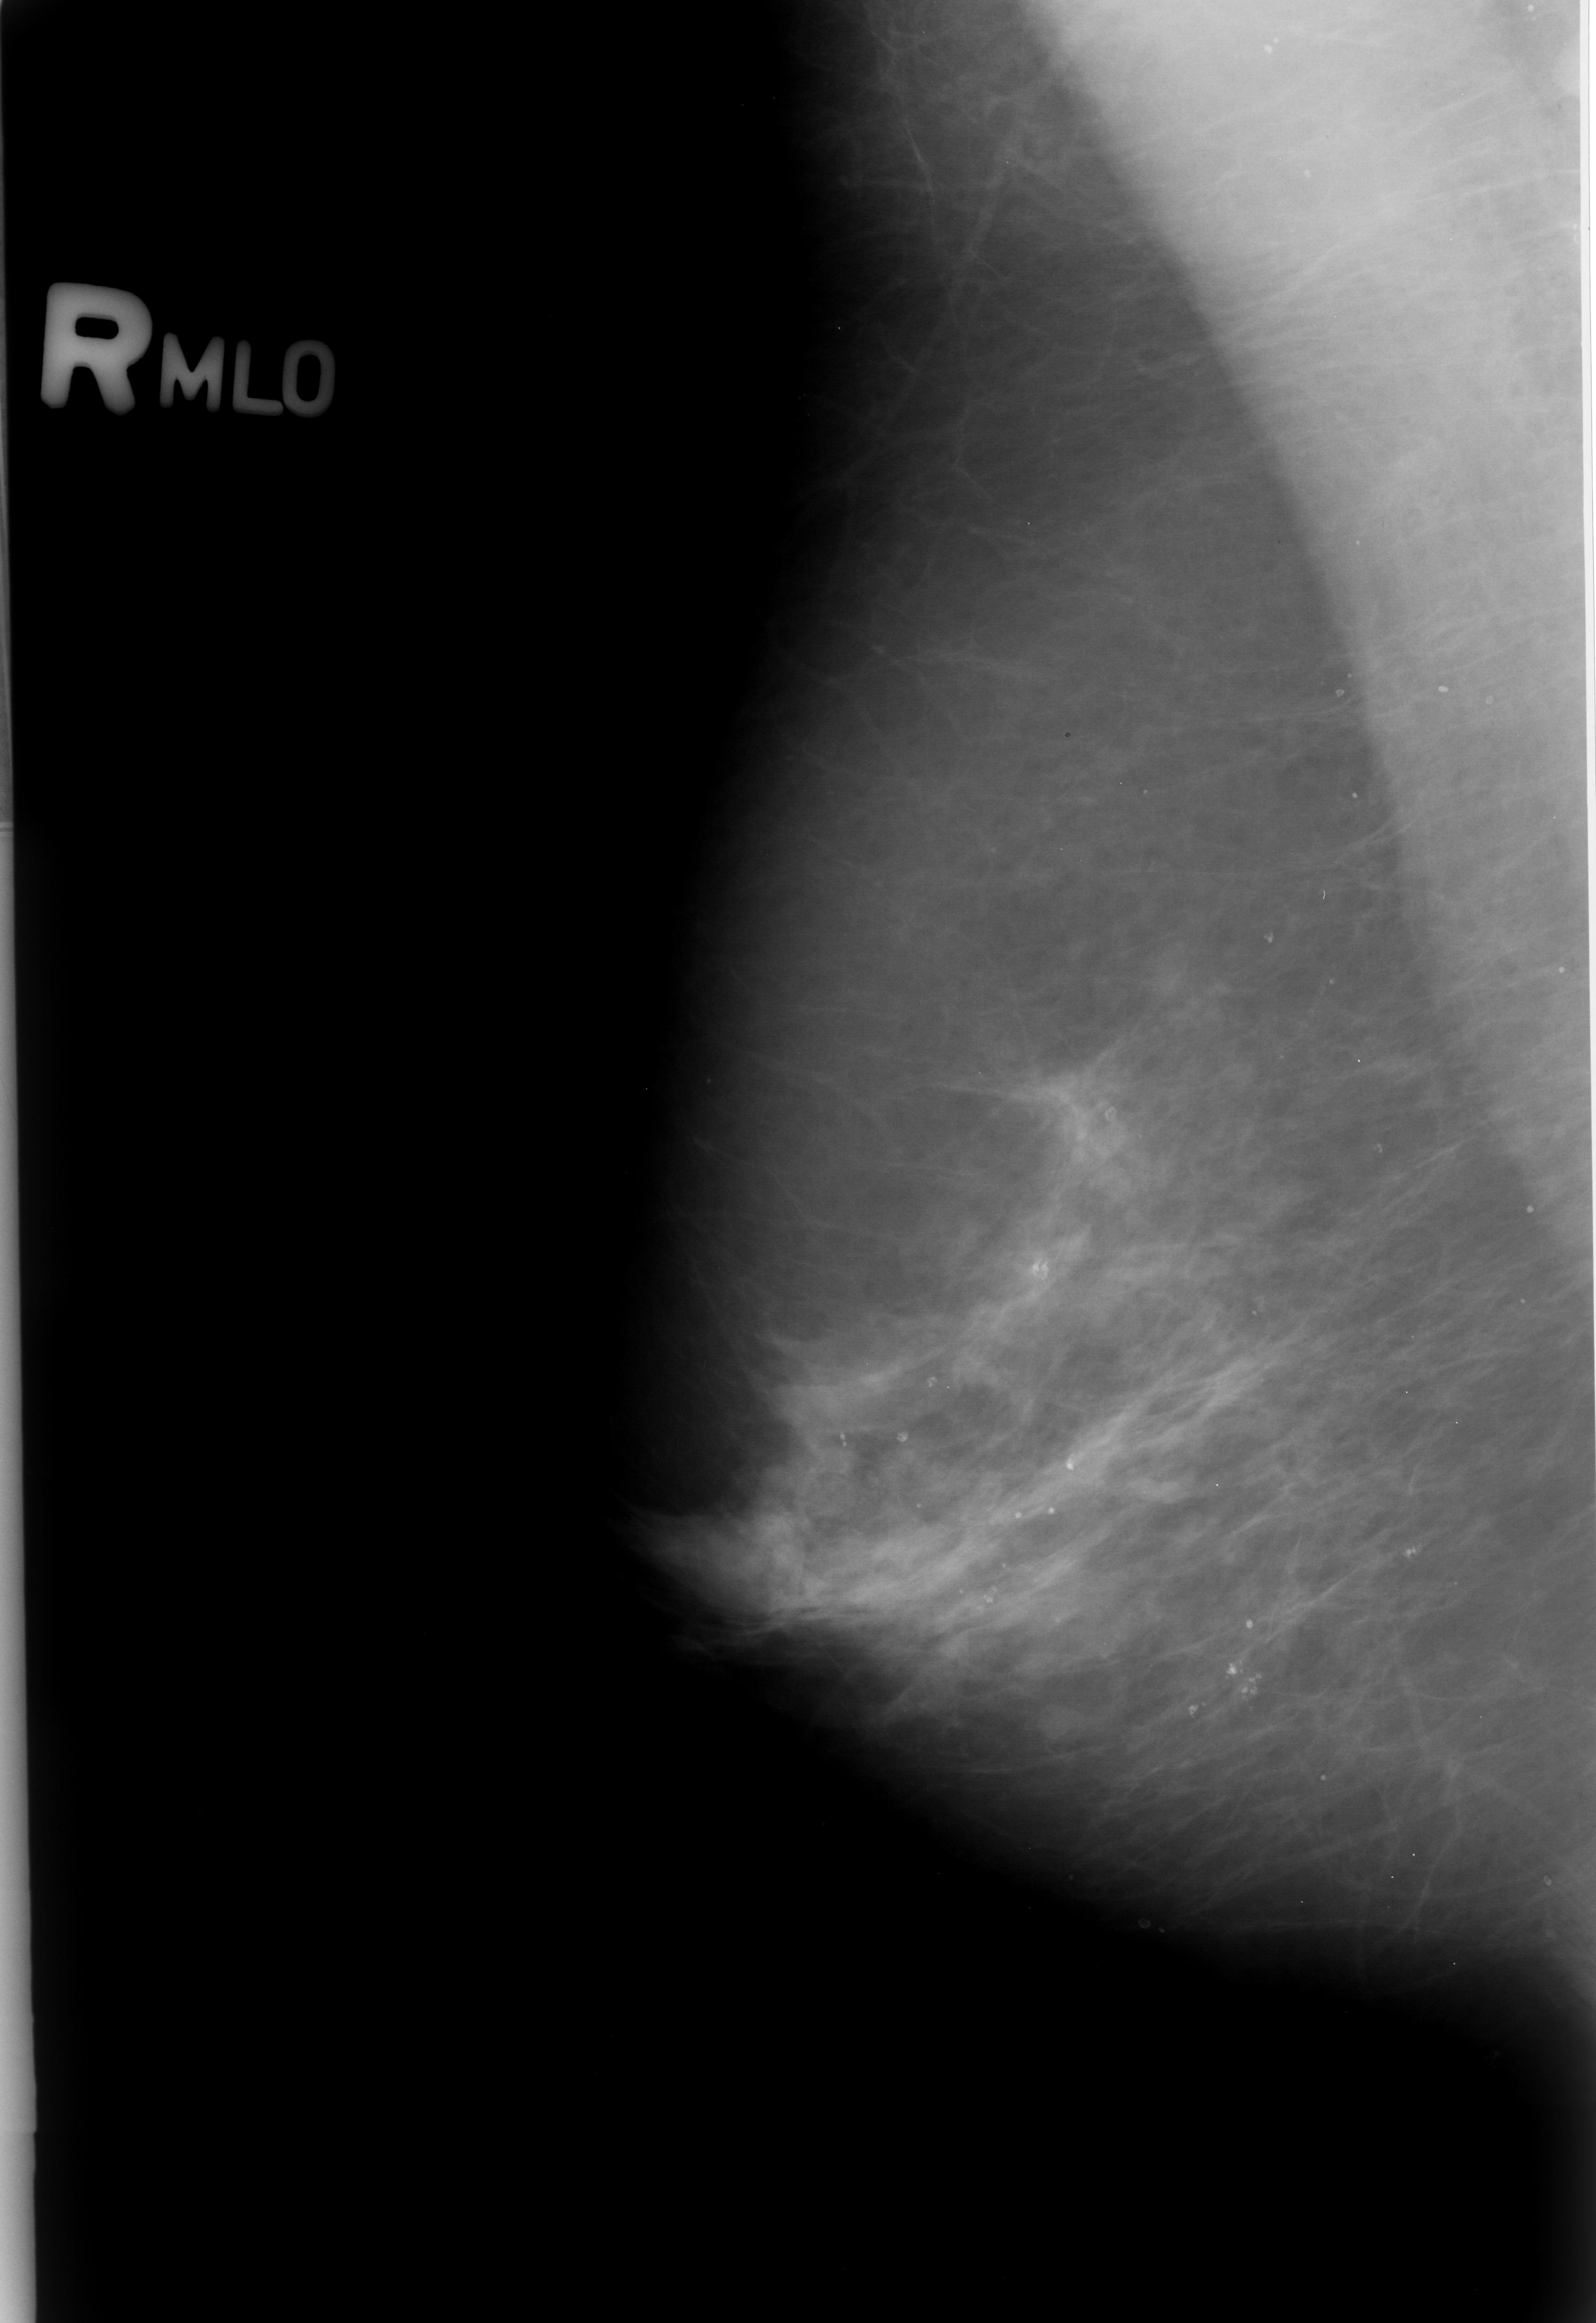
Digitized screen-film mammogram; right breast; MLO view; 1596 × 2323 image matrix.
Expert-marked regions of interest on this film, with their recorded descriptors:
- Finding 1 of 3: calcifications, morphology pleomorphic, distribution clustered; BI-RADS assessment category 2; outcome (as recorded, no biopsy): benign without callback (not worked up further): bounding box (x1, y1, x2, y2) in pixels: (998, 1403, 1112, 1551)
- Finding 2 of 3: calcifications, morphology pleomorphic, distribution clustered; BI-RADS assessment category 2; subtlety rating 4 on a 1 (subtle) to 5 (obvious) scale; outcome (as recorded, no biopsy): benign without callback (not worked up further): (1002, 1211, 1091, 1321)
- Finding 3 of 3: calcifications, morphology pleomorphic, distribution clustered; BI-RADS assessment category 2; subtlety rating 4 on a 1 (subtle) to 5 (obvious) scale; outcome (as recorded, no biopsy): benign without callback (not worked up further): (1174, 1566, 1317, 1735)